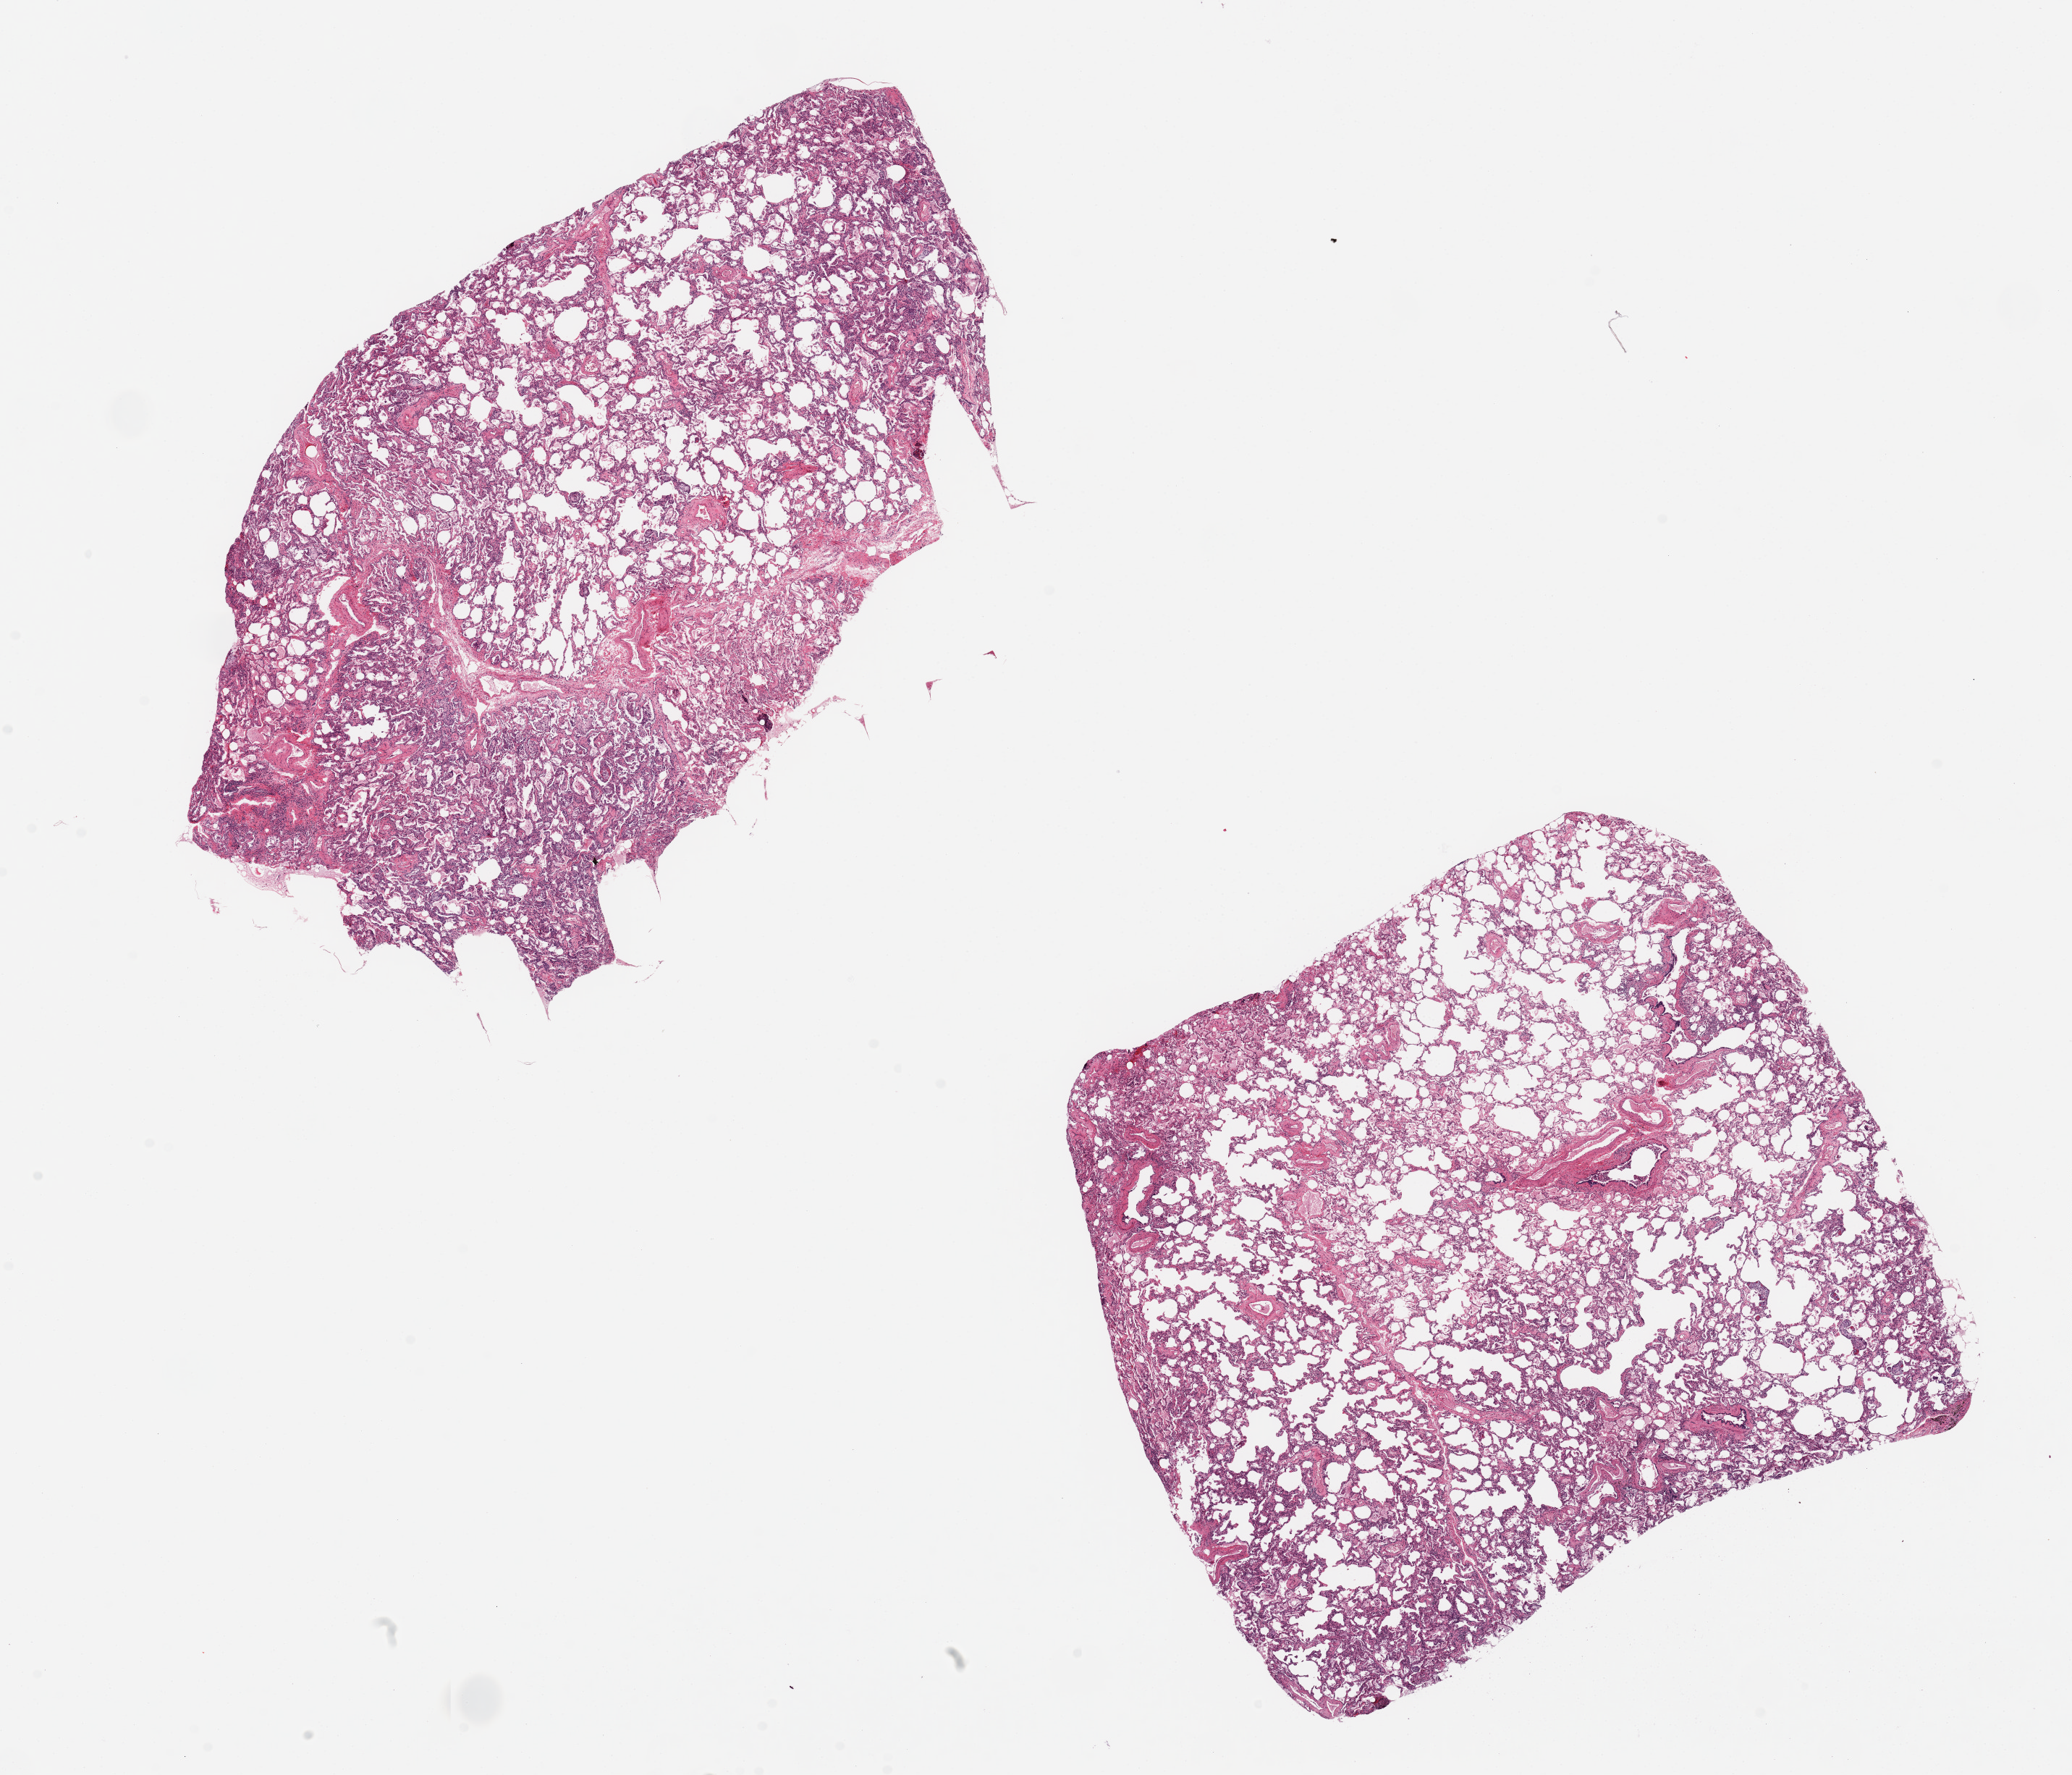
Hematoxylin and eosin (H&E) whole-slide image — low-resolution overview of the scanned area, about 22.6 x 19.4 mm (from a 20x scan). PAXgene-fixed paraffin-embedded (PFPE) section. Sampled site (target tissue): lung. Donor tissue sample. Female donor.
Reviewer comment on this tissue sample: 2 pieces, 11x7 & 8x8mm. Heart failure cells. Focal interstitial fibrosis.